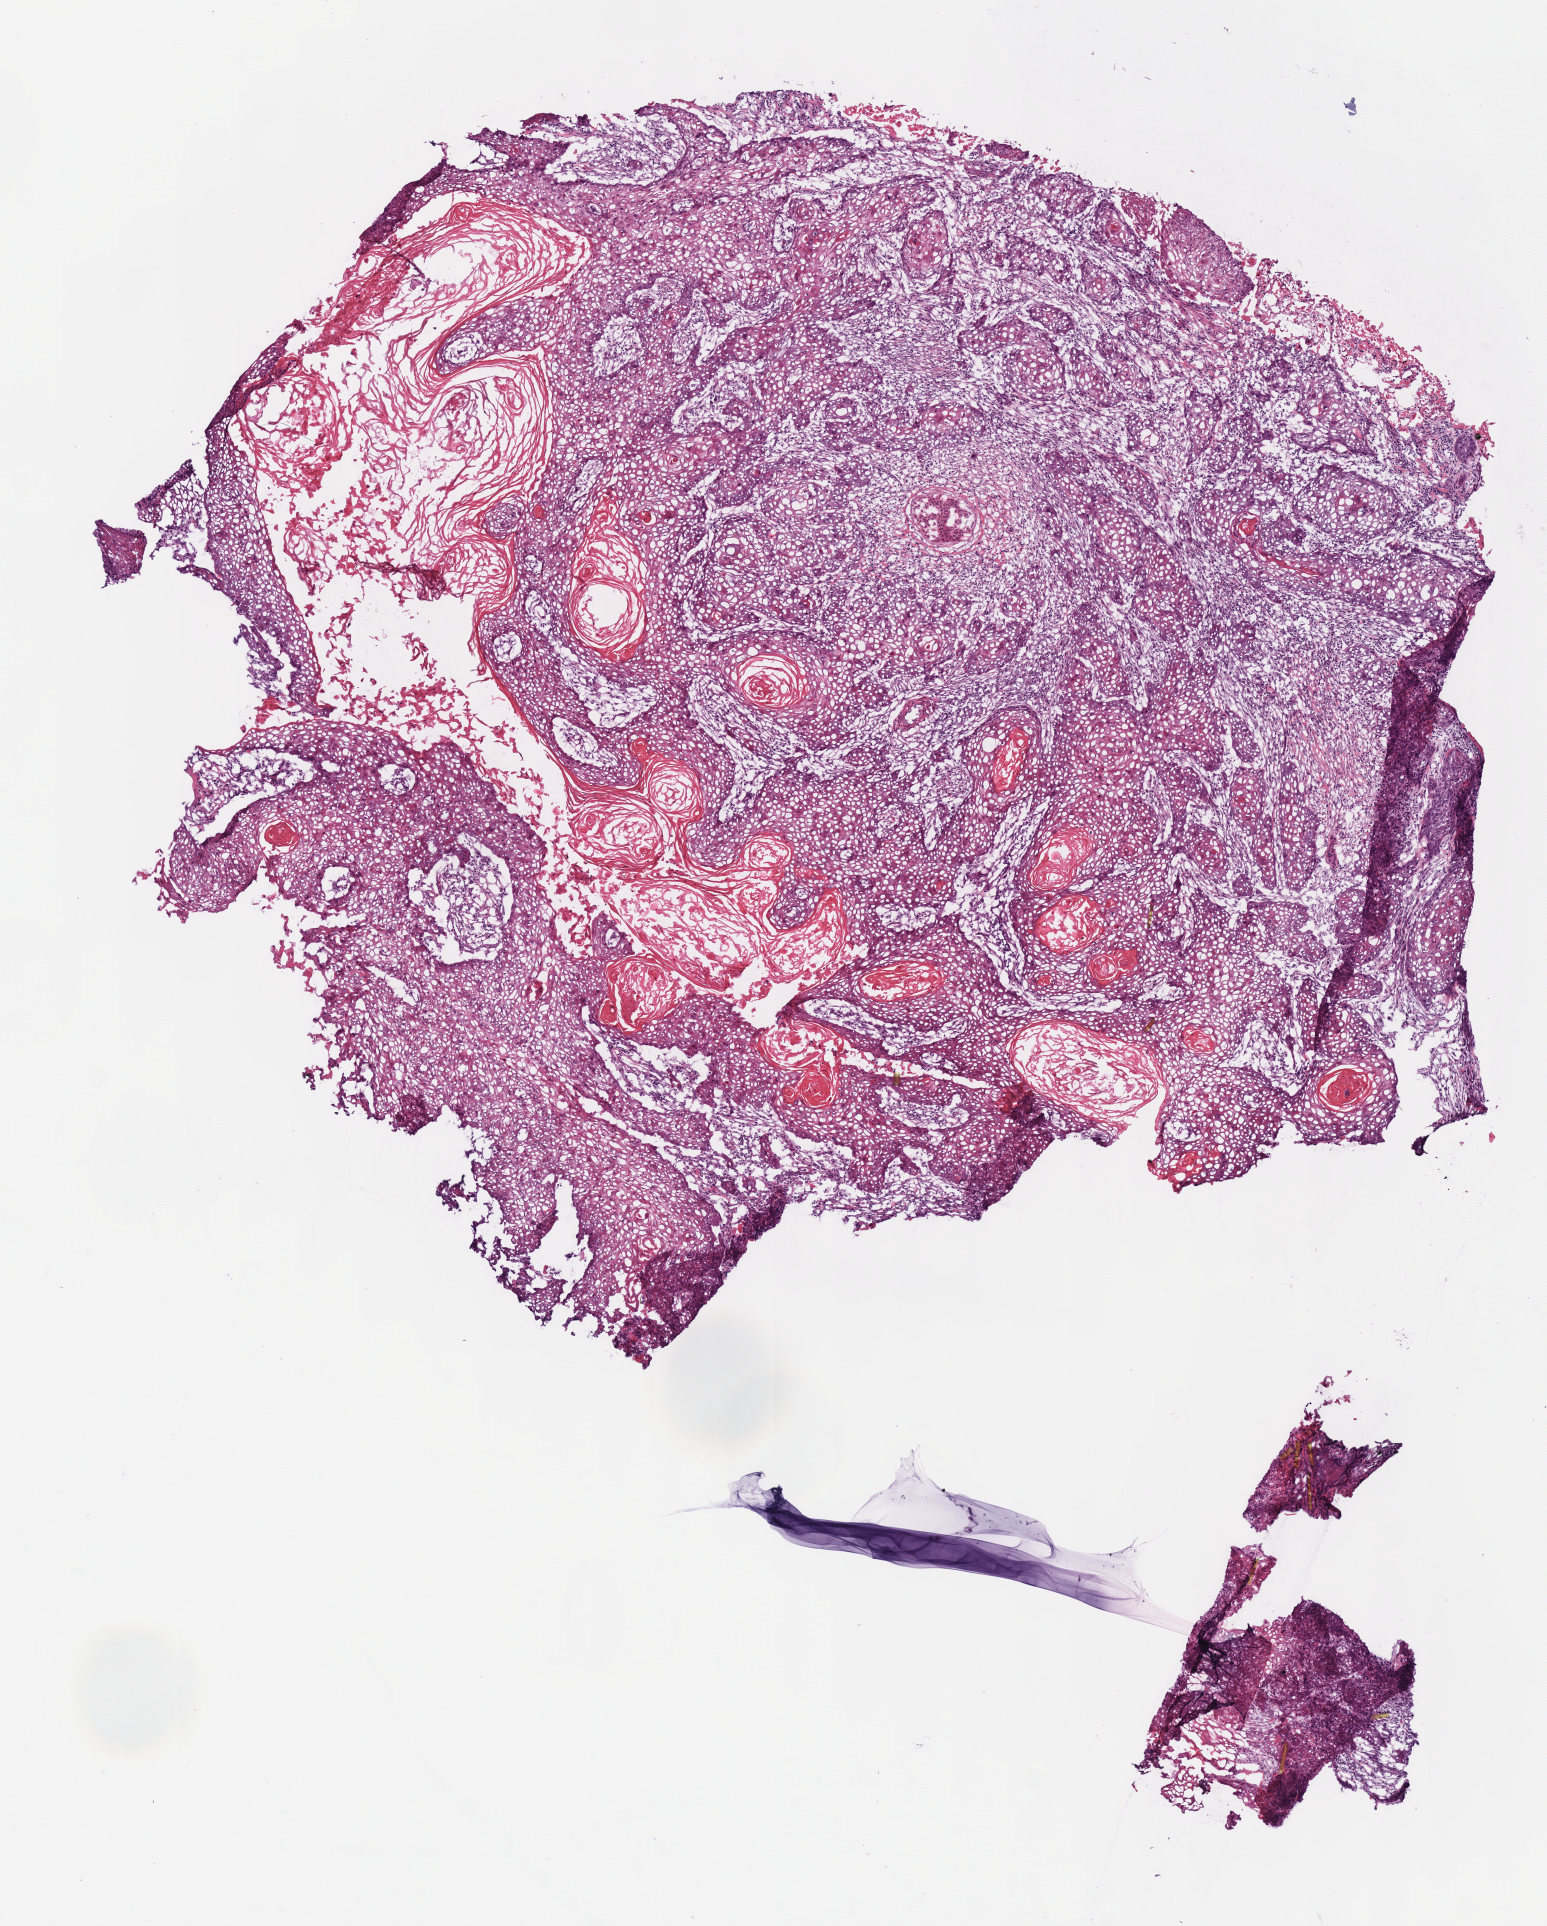
H&E whole-slide image — a low-resolution overview of the entire scanned area, about 6.1 x 7.6 mm. Frozen section from the top of the tissue portion. Sample: primary tumour, head and neck. Patient: female, age at initial diagnosis 74 years. Histologic grade: G2 (moderately differentiated). Composition of this section per pathologist review: tumour cells 96%, tumour nuclei 75%, normal cells 0%, stromal cells 4%, necrosis 0%. Infiltration values recorded for this section: lymphocyte infiltration 15%, monocyte infiltration 0%, neutrophil infiltration 4%.
Histologic diagnosis: Squamous cell carcinoma, NOS. Laterality: right. AJCC pathologic stage: II (7th edition).